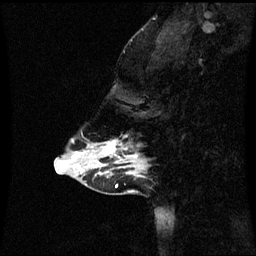
Breast MRI (dynamic contrast-enhanced), one sagittal slice. Slice 16 of 60 in the series (ordered by position). Dynamic contrast-enhanced series, image 2 of 3 at this slice position (ordered by acquisition). 1.5 T. TE 4.2 ms, TR 8.9 ms. 2 mm slice thickness. 256 × 256 image matrix, field of view 220 × 220 mm. Female patient, age 43 years. From the clinical record (not read from this slice): setting: breast cancer imaged before/during neoadjuvant chemotherapy; receptor status: HR-positive, HER2-negative.
Outlined on this slice (semi-automatic segmentation, software-assisted and operator-edited):
- analysis volume of interest (the breast-tissue region the enhancement analysis was run in; not a lesion): bounding box [x1, y1, x2, y2] px = [84, 142, 144, 171]
- tumour enhancement mask (voxels above the 70 % enhancement threshold inside the analysis volume of interest): [103, 142, 137, 163]